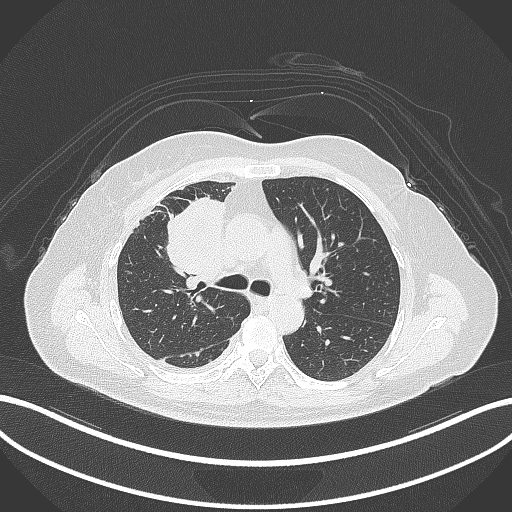
Chest CT, one axial slice; reconstruction kernel B70f; lung window (W 1500 / L -600 HU); 512 × 512 image matrix. Female patient, age 52 years. From the clinical record (not read from this slice): clinical TNM (as recorded): T3 N1 M1.
Outlined on this slice (rectangle marked by the reading radiologist):
- lung tumour (recorded histology: adenocarcinoma): box from (x=153, y=186) to (x=230, y=280) px